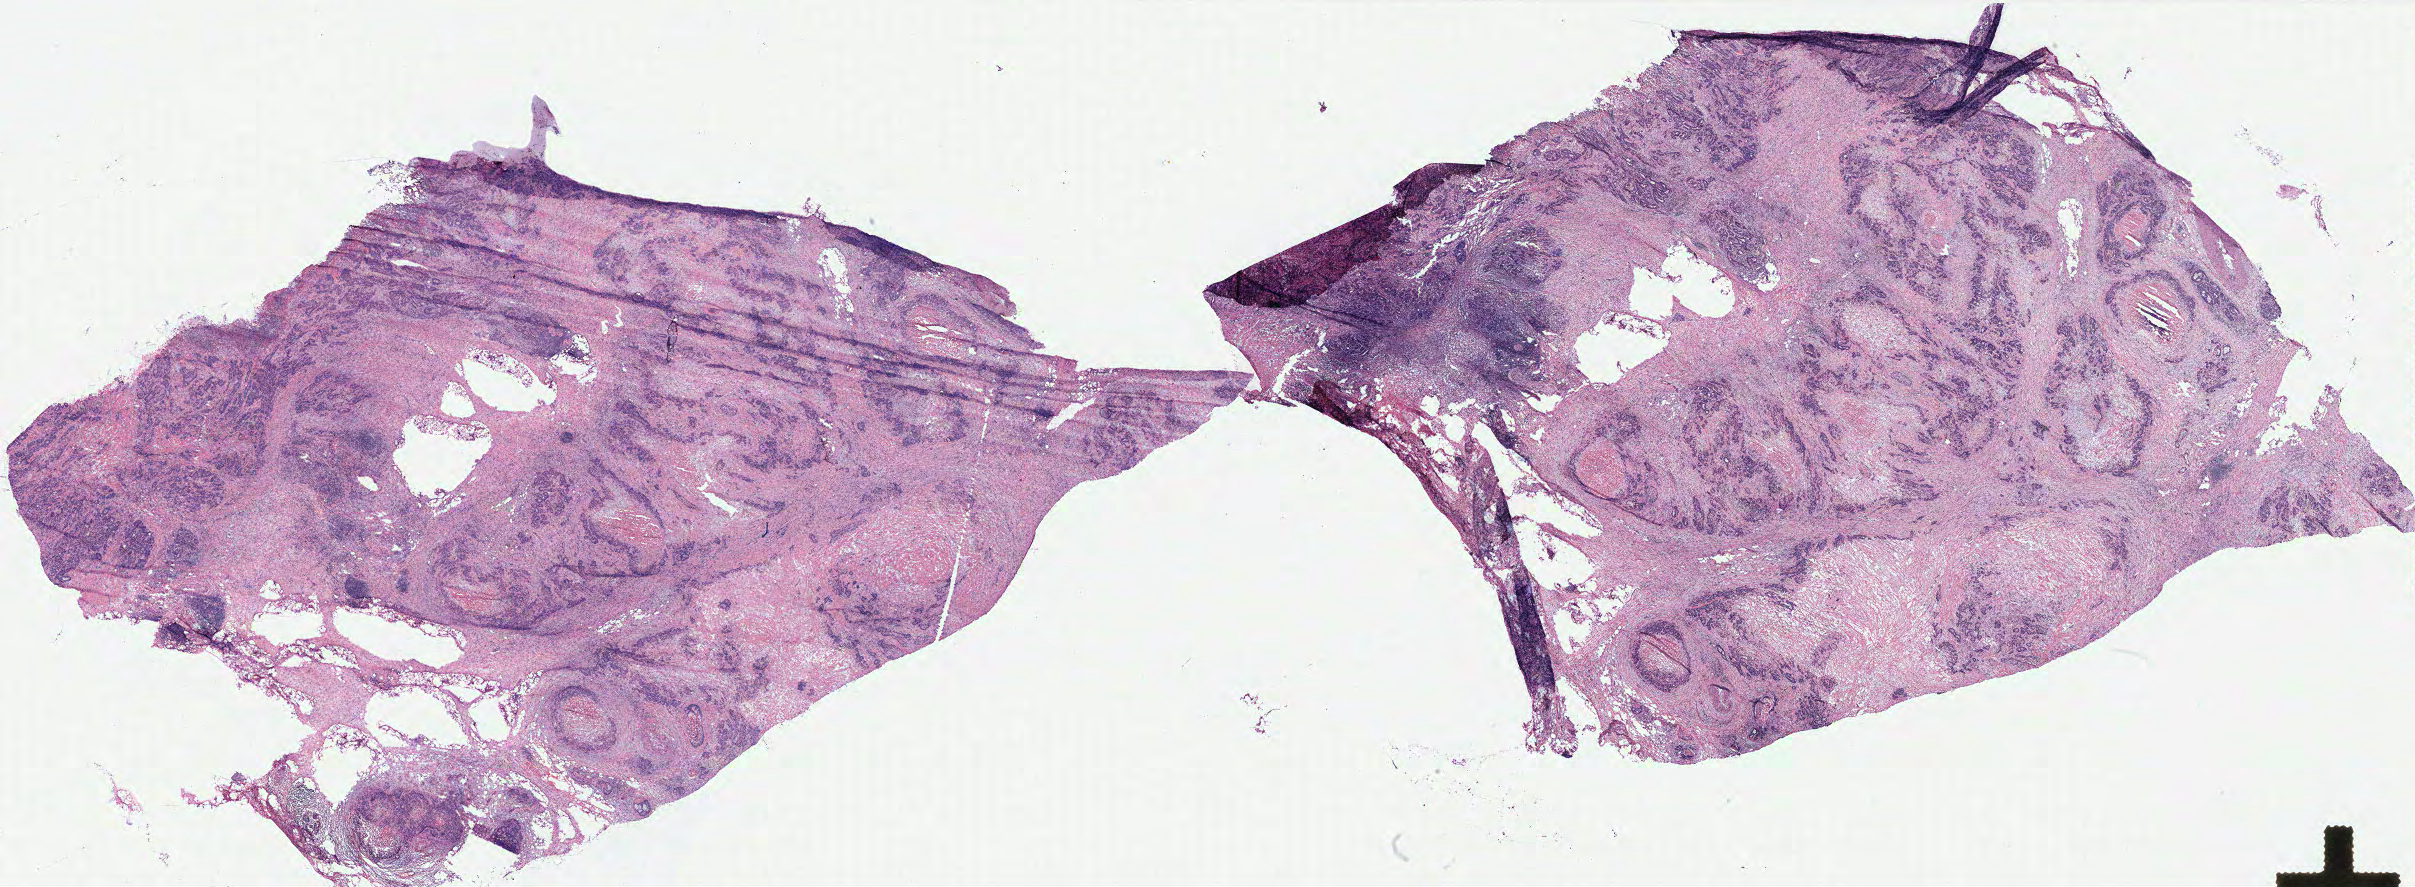
H&E whole-slide image, shown as a low-resolution overview of the whole scanned area (about 38.7 x 14.2 mm), colon, tissue type not recorded.
Patient diagnosis (cohort enrolment): colon cancer (colon).